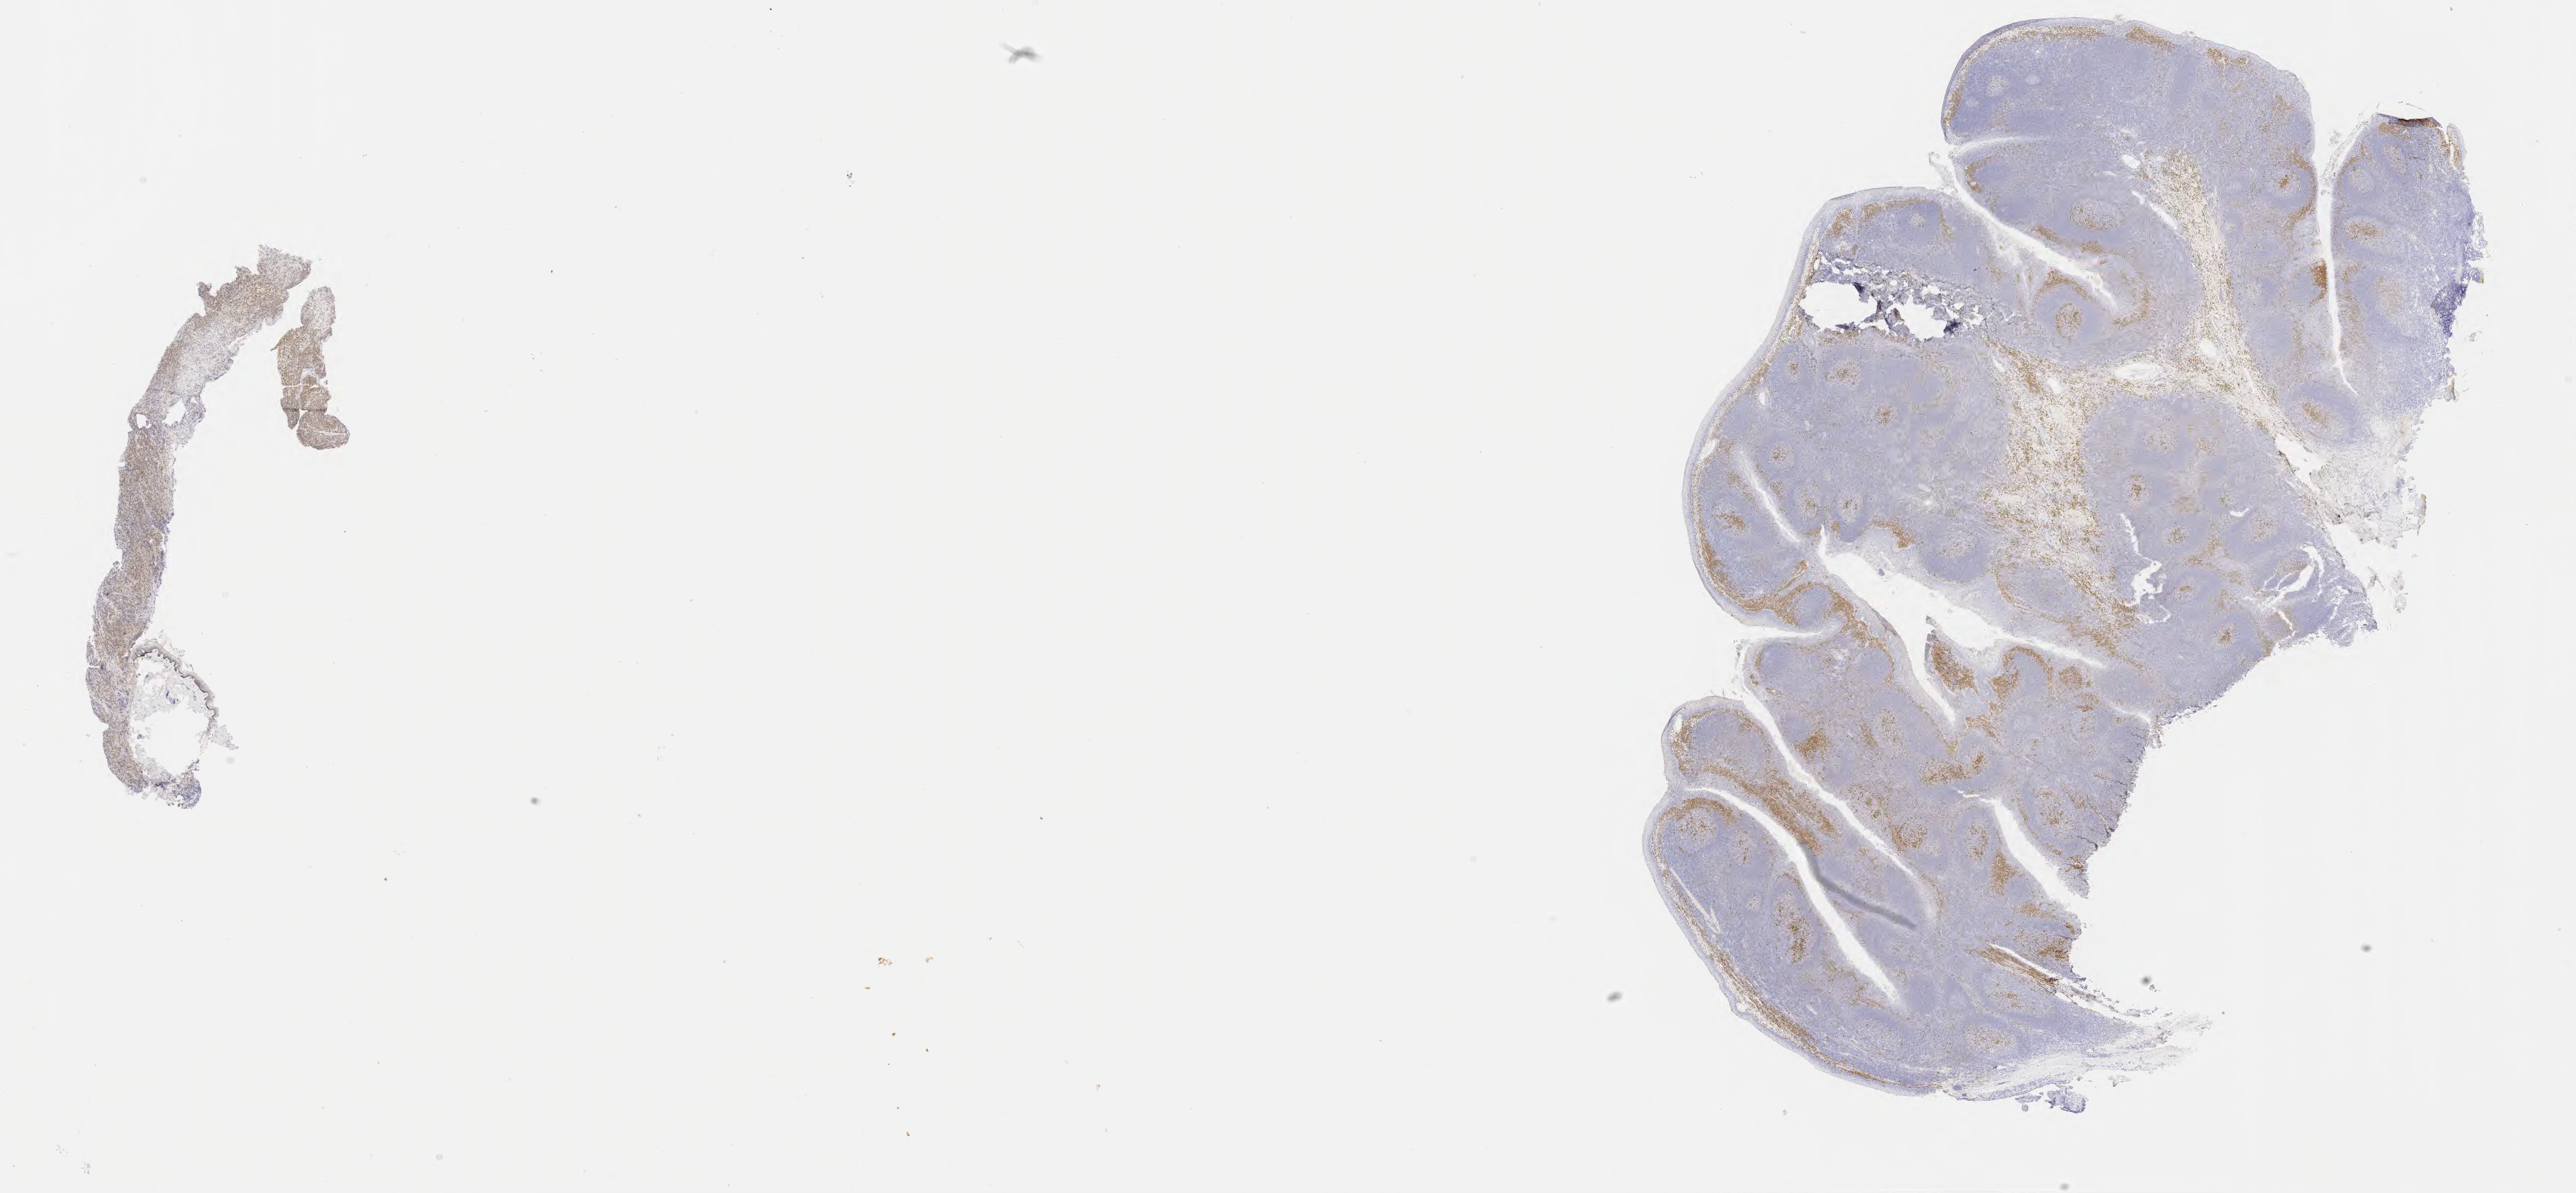
Whole-slide image, immunohistochemical stain for IRF4/MUM1 — shown as a low-resolution overview of the whole scanned area (about 29.2 x 13.5 mm); specimen: tumor tissue. Patient: female, aged 43.
Histologic diagnosis: Diffuse large B-cell lymphoma, NOS.